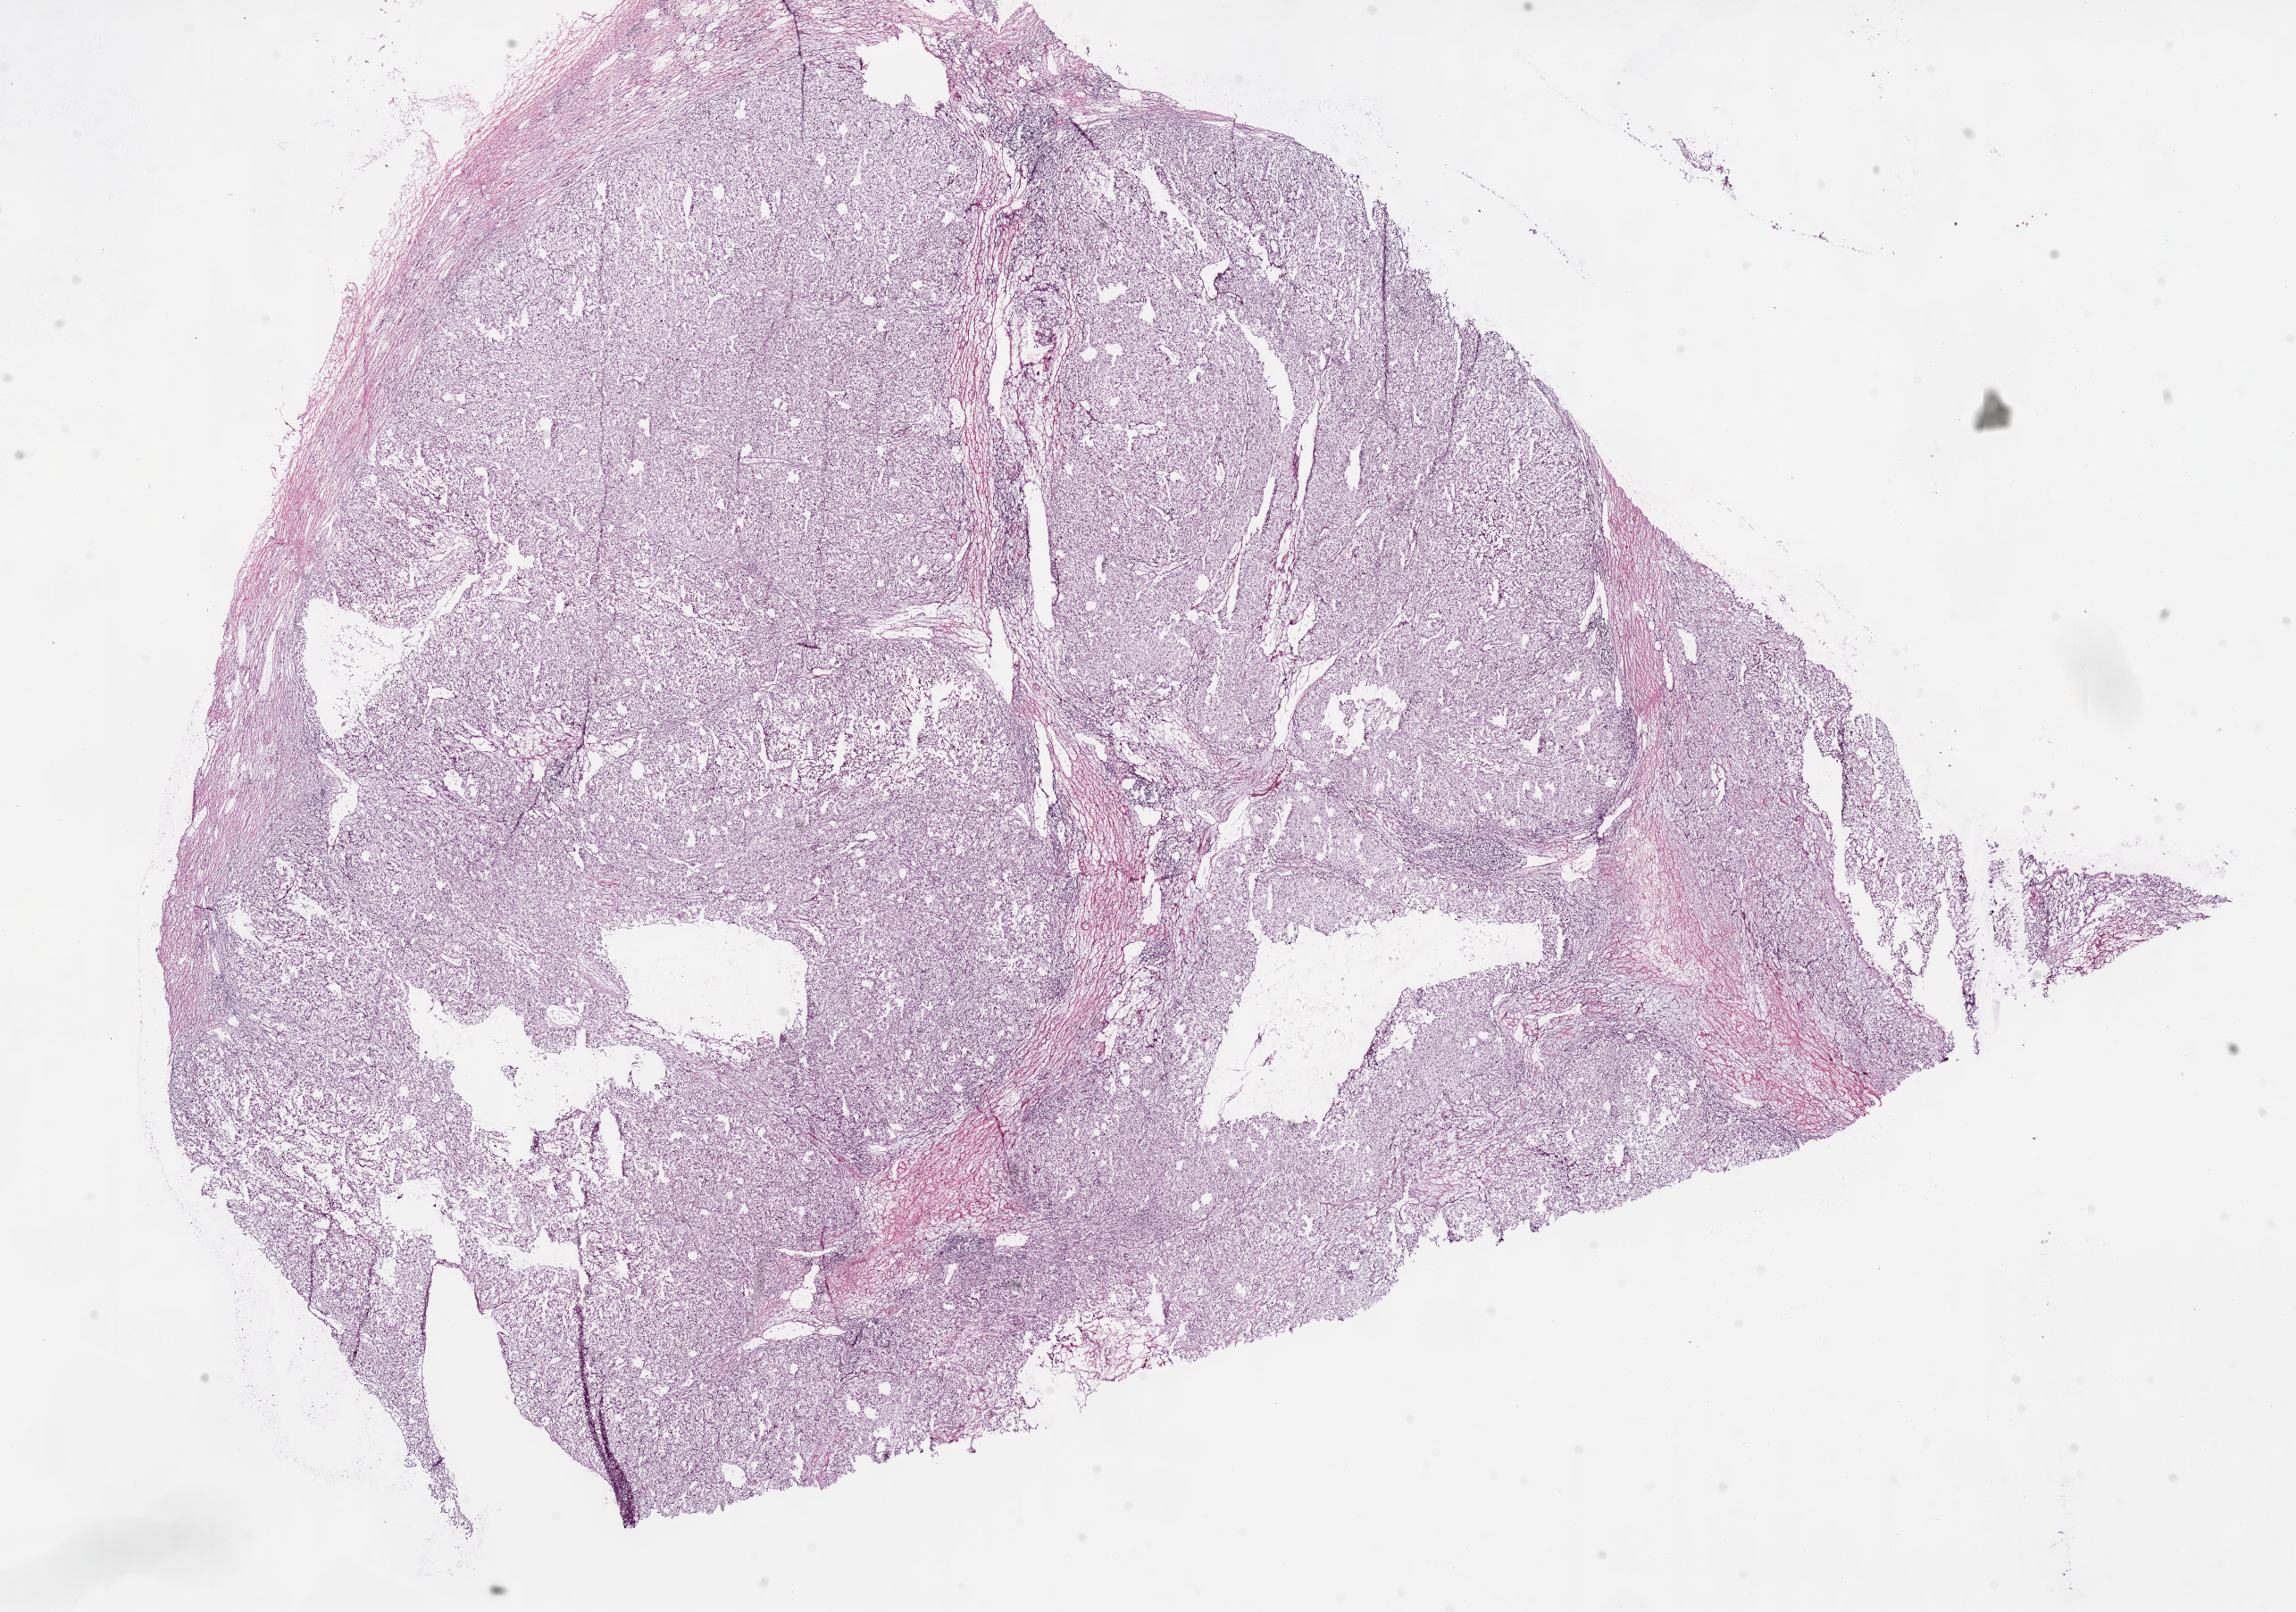
Hematoxylin and eosin (H&E) stained whole-slide image — low-resolution overview of the scanned area, about 20.6 x 14.5 mm (slide scanned at 5x); frozen section; kidney, primary tumour sample. Male, age 55 years at initial diagnosis. Histologic grade: G3 (poorly differentiated). Slide review estimates, as recorded: tumour cells 85%, tumour nuclei 80%, normal cells 0%, stromal cells 15%, necrosis 0%.
Diagnosis: Clear cell adenocarcinoma, NOS. Laterality: left. TNM: T2 N0 M1. AJCC pathologic stage: IV.